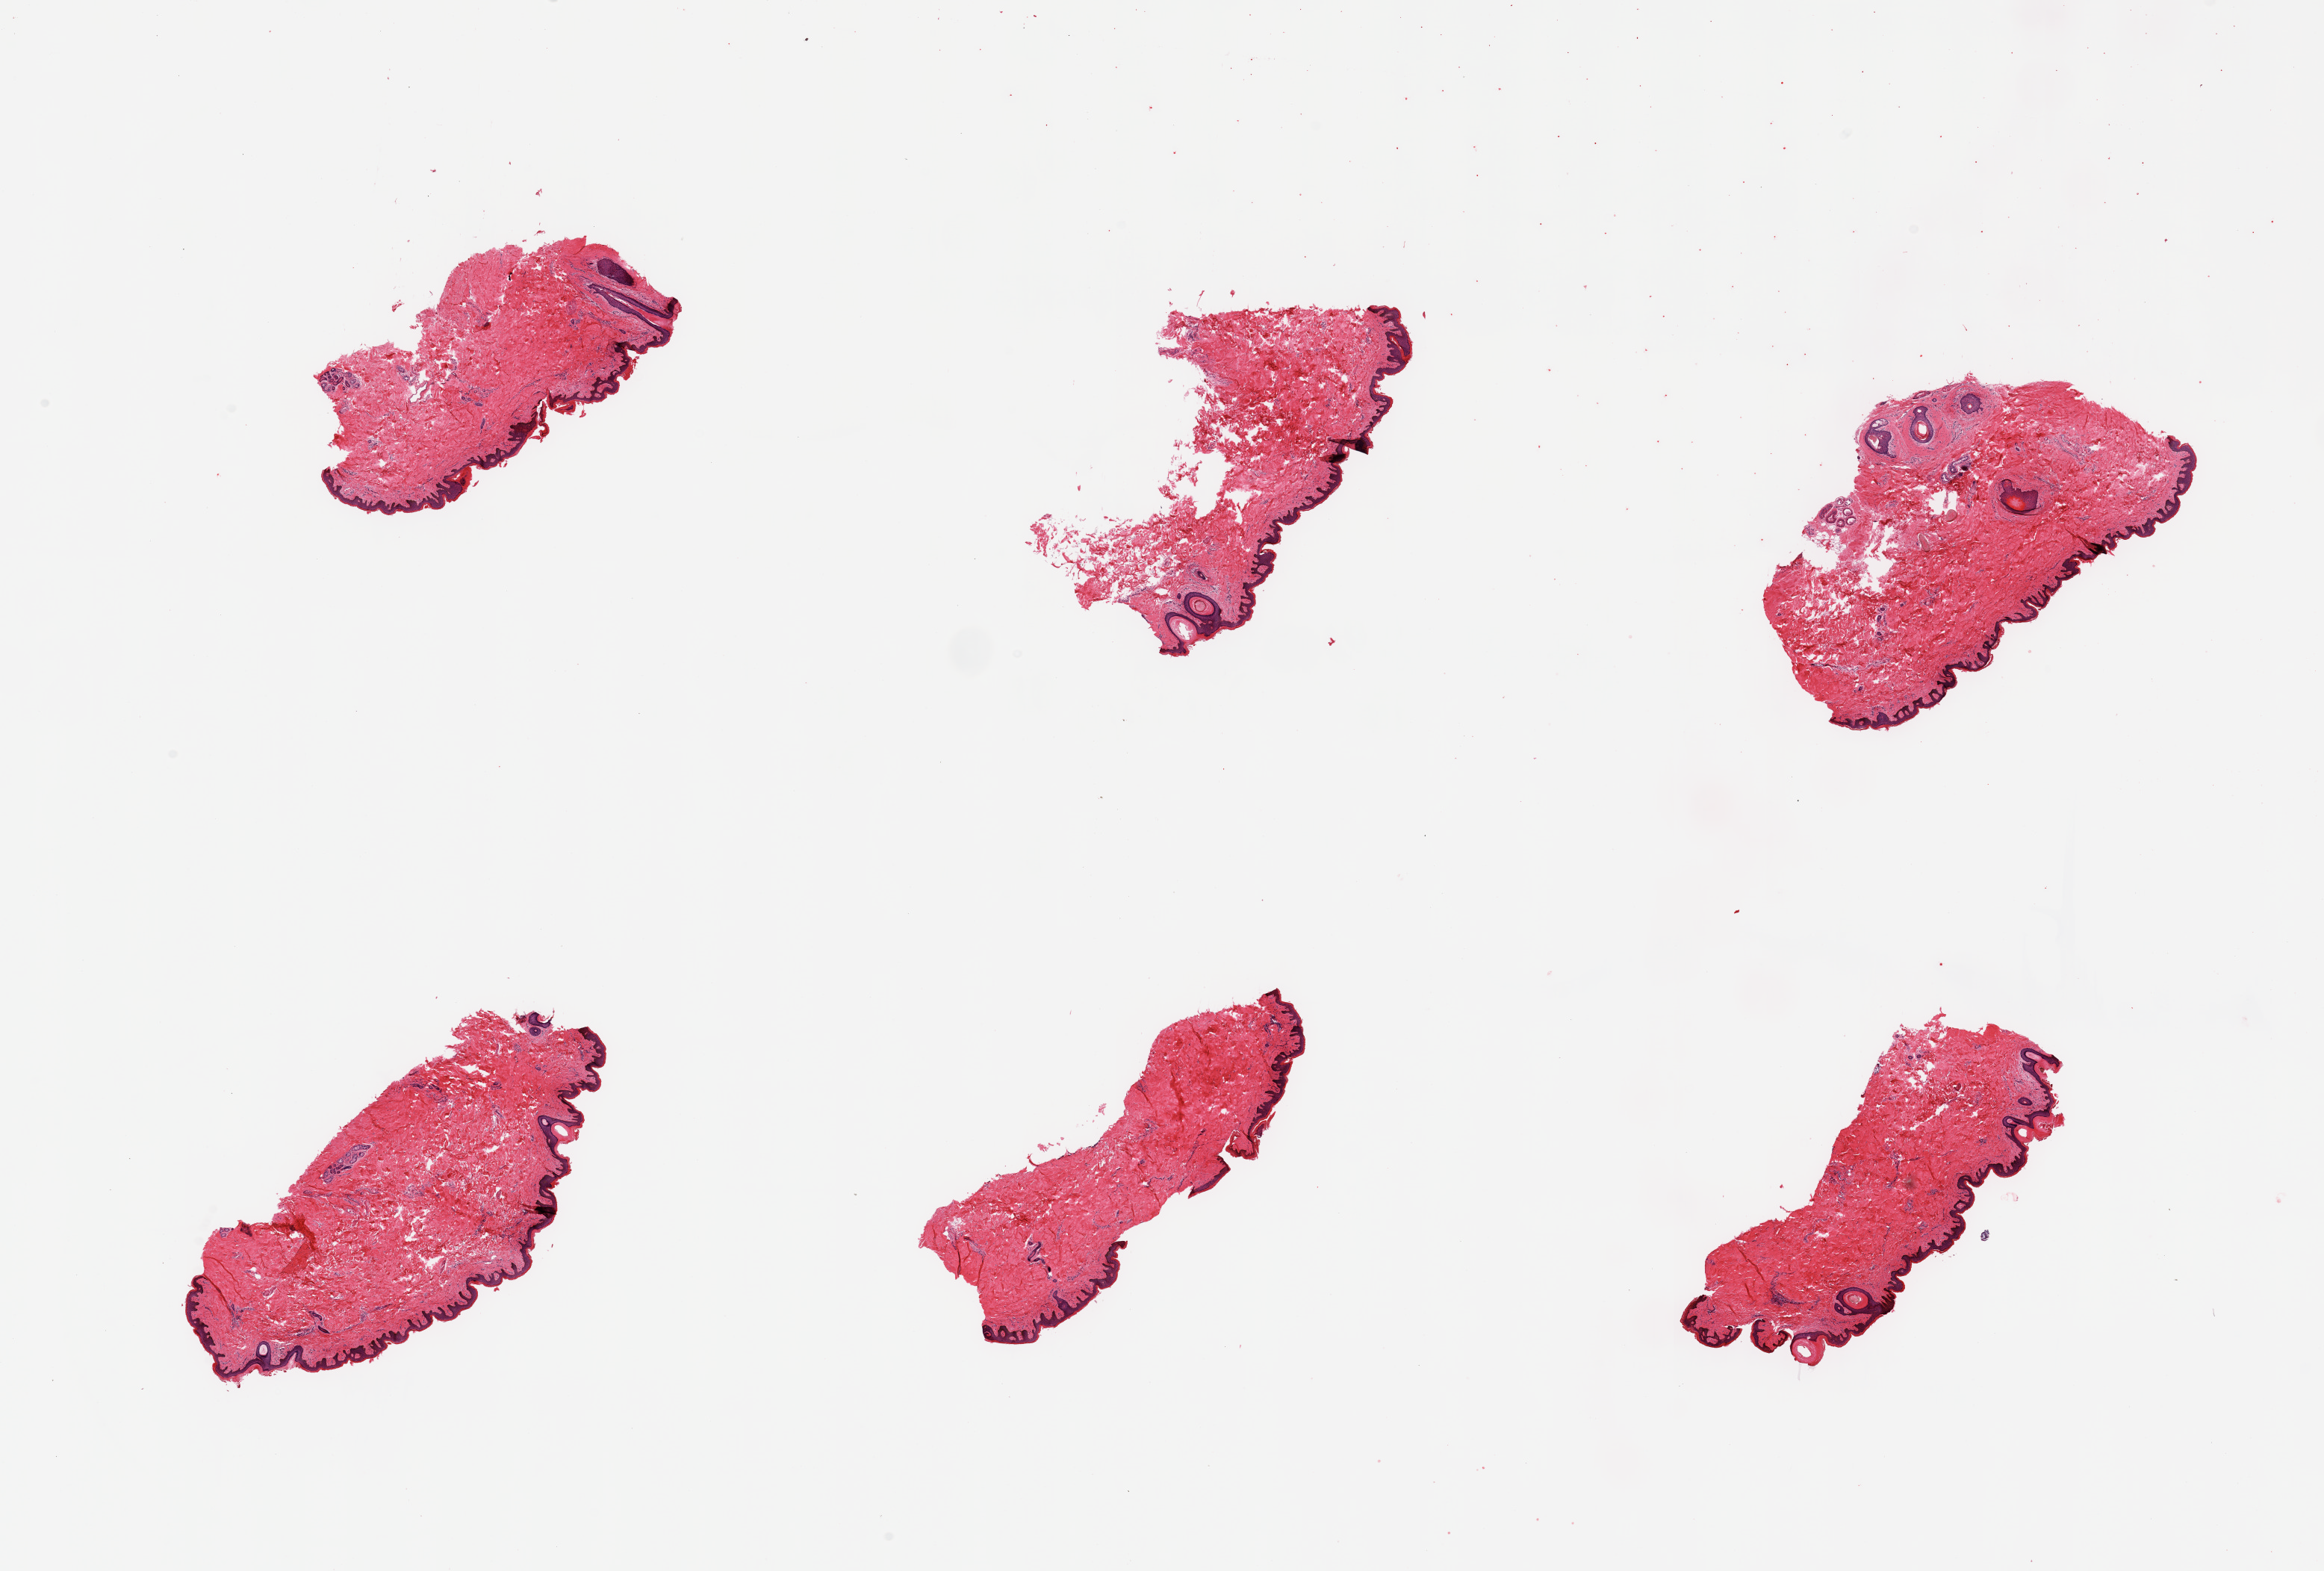
Haematoxylin and eosin whole-slide image — shown as a low-resolution overview of the whole scanned area (about 24.6 x 16.6 mm, from a 20x scan). PAXgene-fixed paraffin-embedded (PFPE) section. Section of skin of suprapubic region (target tissue). Tissue donor sample. Donor: male.
Review note (as recorded): 6 pieces; well trimmed.